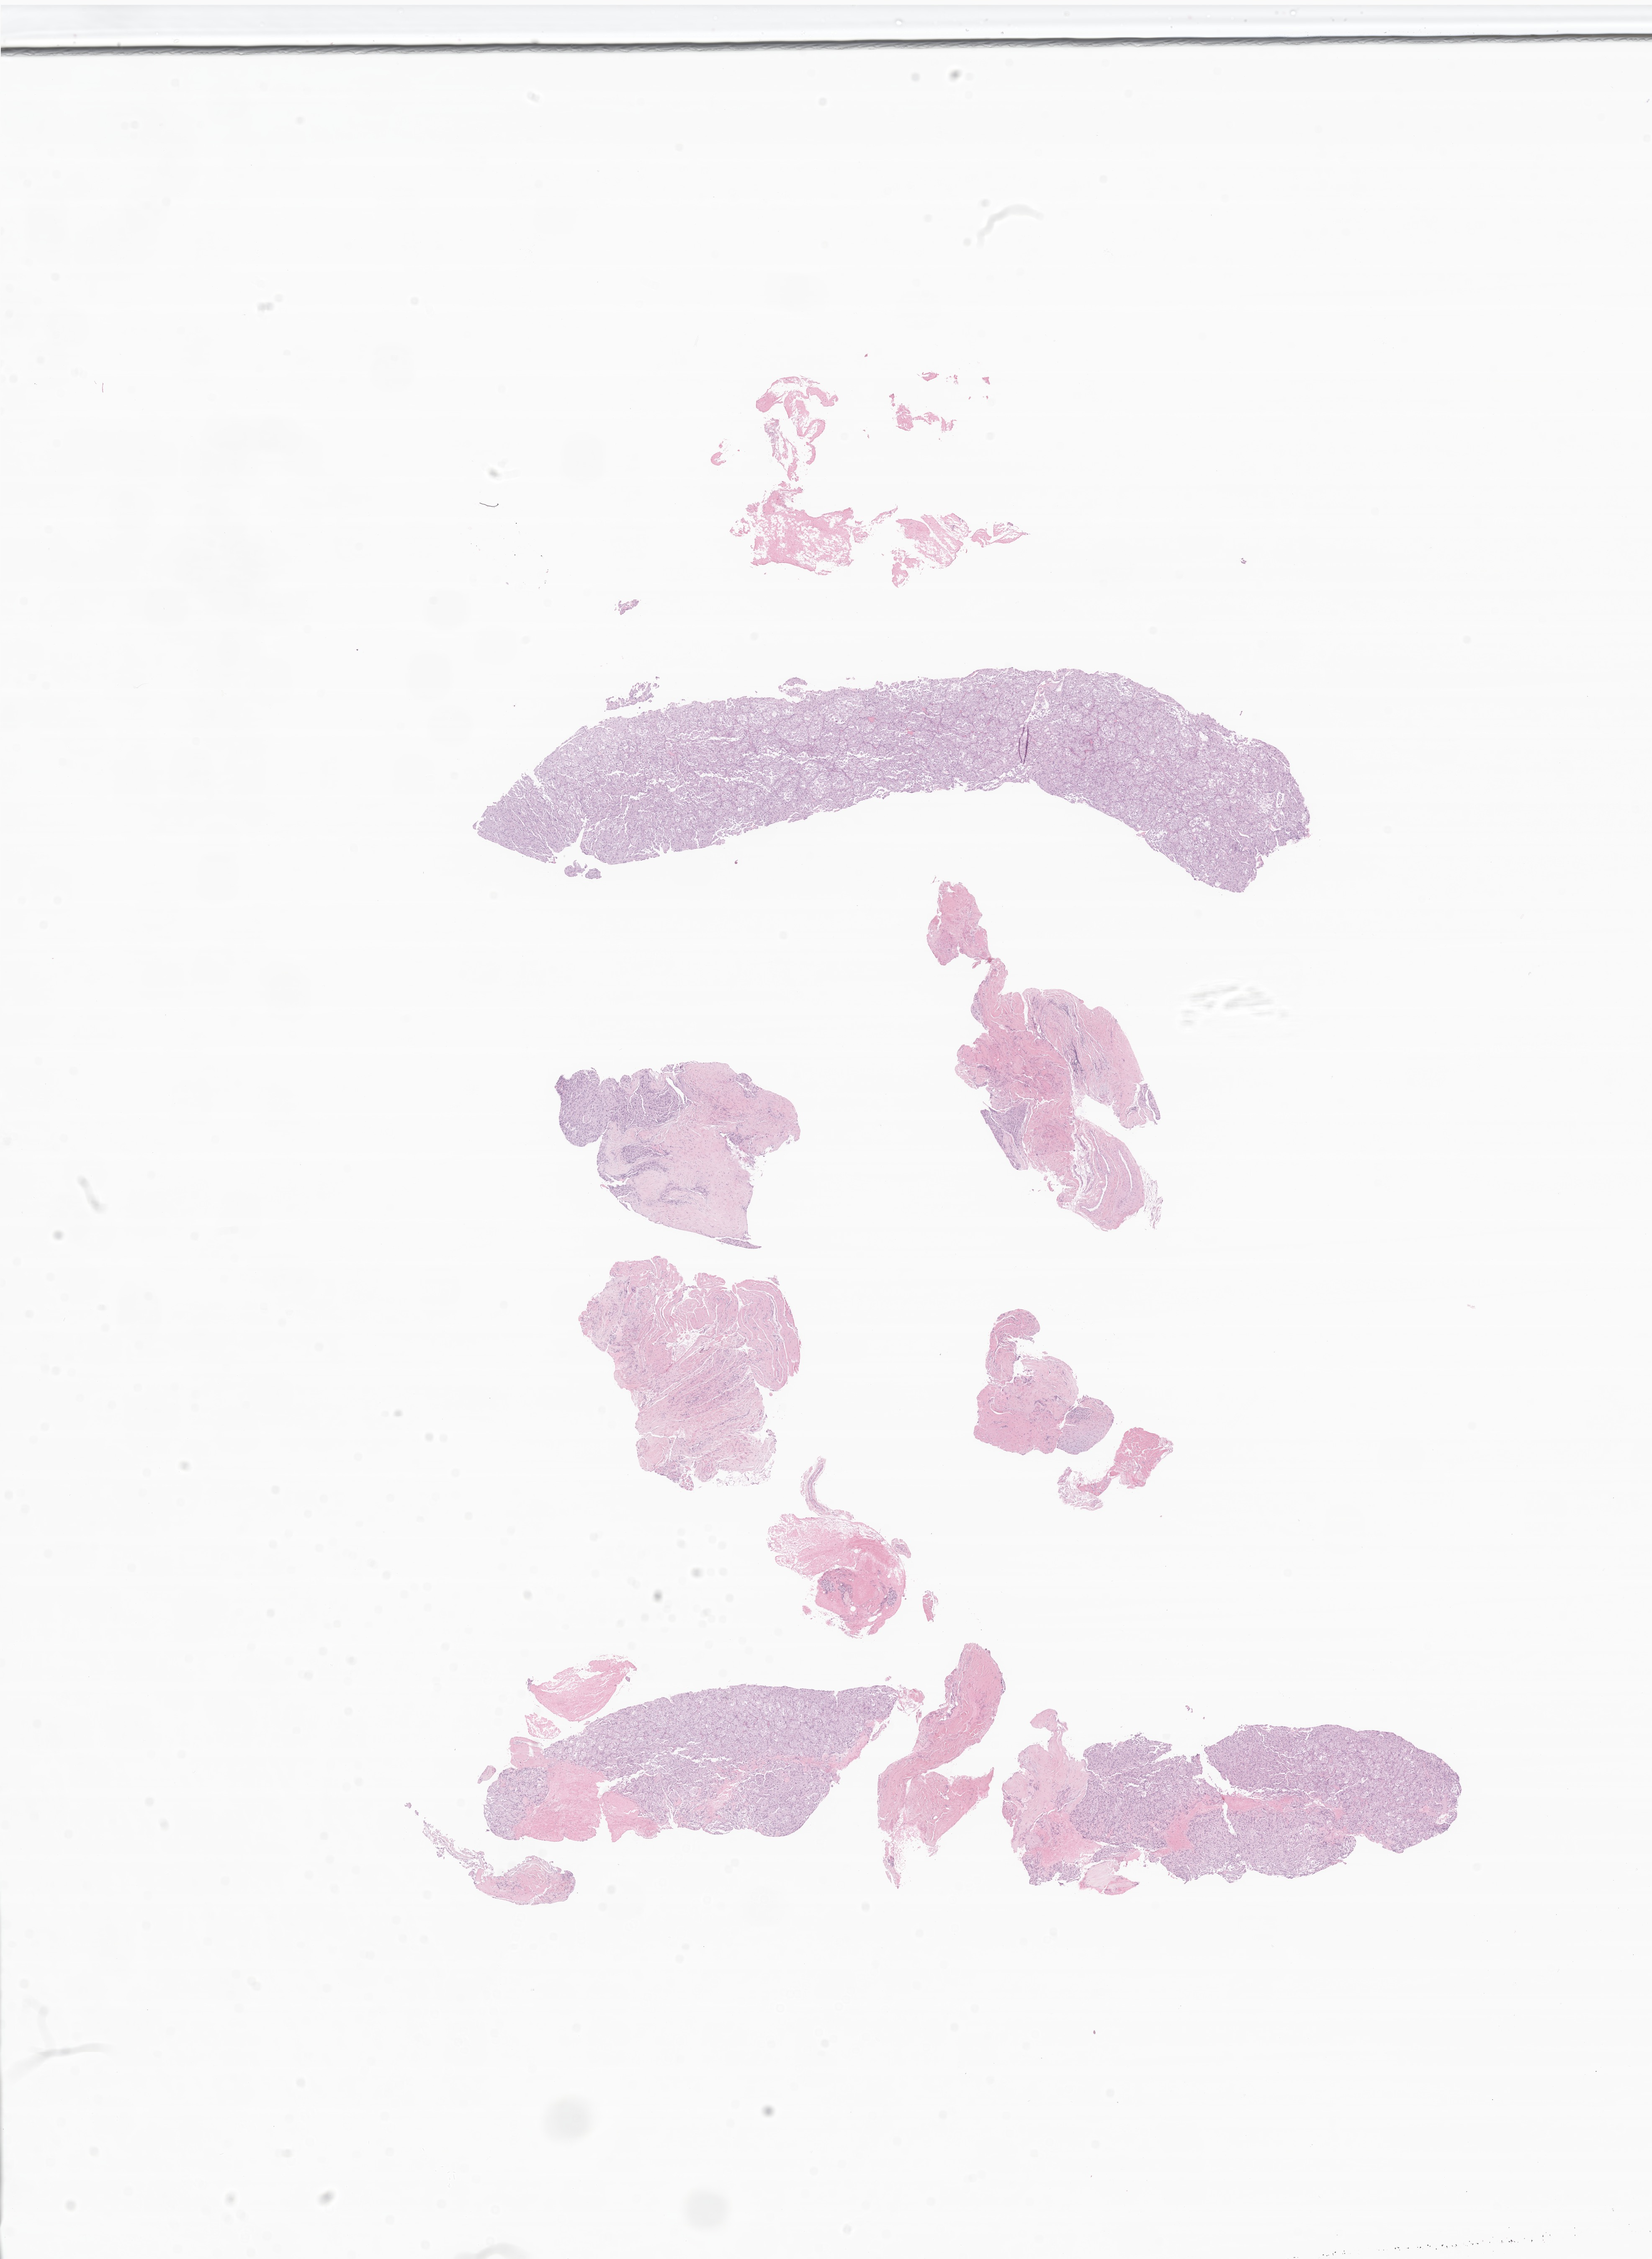
Whole-slide image, hematoxylin and eosin (H&E) stain of tumor tissue from the lower limb — low-resolution overview of the scanned area, about 16.6 x 22.7 mm; FFPE section. Female patient, age 66 months (5 years 6 months).
Diagnosis: Alveolar soft part sarcoma.